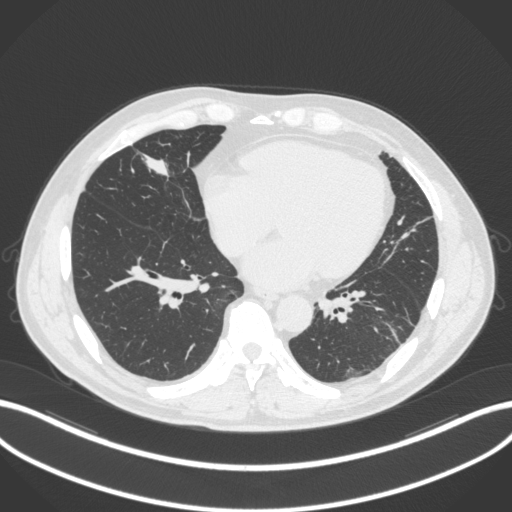
Chest CT, one axial slice; lung window (W 1500 / L -600 HU); 1 mm slice thickness; 512 × 512 image matrix. Patient: male, 59 years. Case-level facts recorded for this patient, not image findings: clinical TNM (as recorded): T2a N1 M0.
Annotated regions visible in this slice (bounding box drawn by a radiologist):
- lung tumour (recorded histology: adenocarcinoma): box from (x=134, y=143) to (x=171, y=185) px